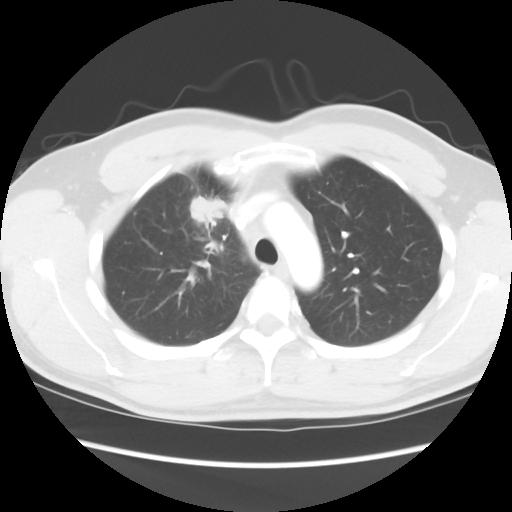
Chest CT, one axial slice. Slice 66 of 80 in the series (ordered by position). 120 kVp. Lung window (W 1500 / L -600 HU). 512 × 512 image matrix, field of view 360 × 360 mm. Patient: male, 35 years. Case-level facts recorded for this patient, not image findings: clinical TNM (as recorded): T1c N1 M1b.
Annotated regions visible in this slice (bounding box drawn by a radiologist):
- lung tumour (recorded histology: adenocarcinoma): bounding box [x1, y1, x2, y2] px = [184, 190, 232, 226]